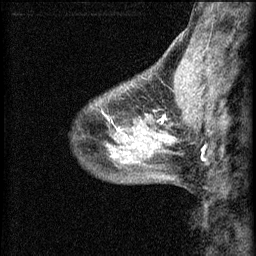
Breast MRI (dynamic contrast-enhanced), one sagittal slice; slice 20 of 60 in the series (ordered by position); 3 images stored at this slice position (order not interpretable as contrast timing); 1.5 T; TE 4.2 ms, TR 8.2 ms; 2.2 mm slice thickness; 256 × 256 image matrix, field of view 180 × 180 mm. Patient: female, 40 years.
Outlined on this slice (semi-automatic segmentation, software-assisted and operator-edited):
- analysis volume of interest (the breast-tissue region the enhancement analysis was run in; not a lesion): box from (x=108, y=82) to (x=175, y=139) px
- tumour enhancement mask (voxels above the 70 % enhancement threshold inside the analysis volume of interest): (x=112, y=116)–(x=167, y=137)